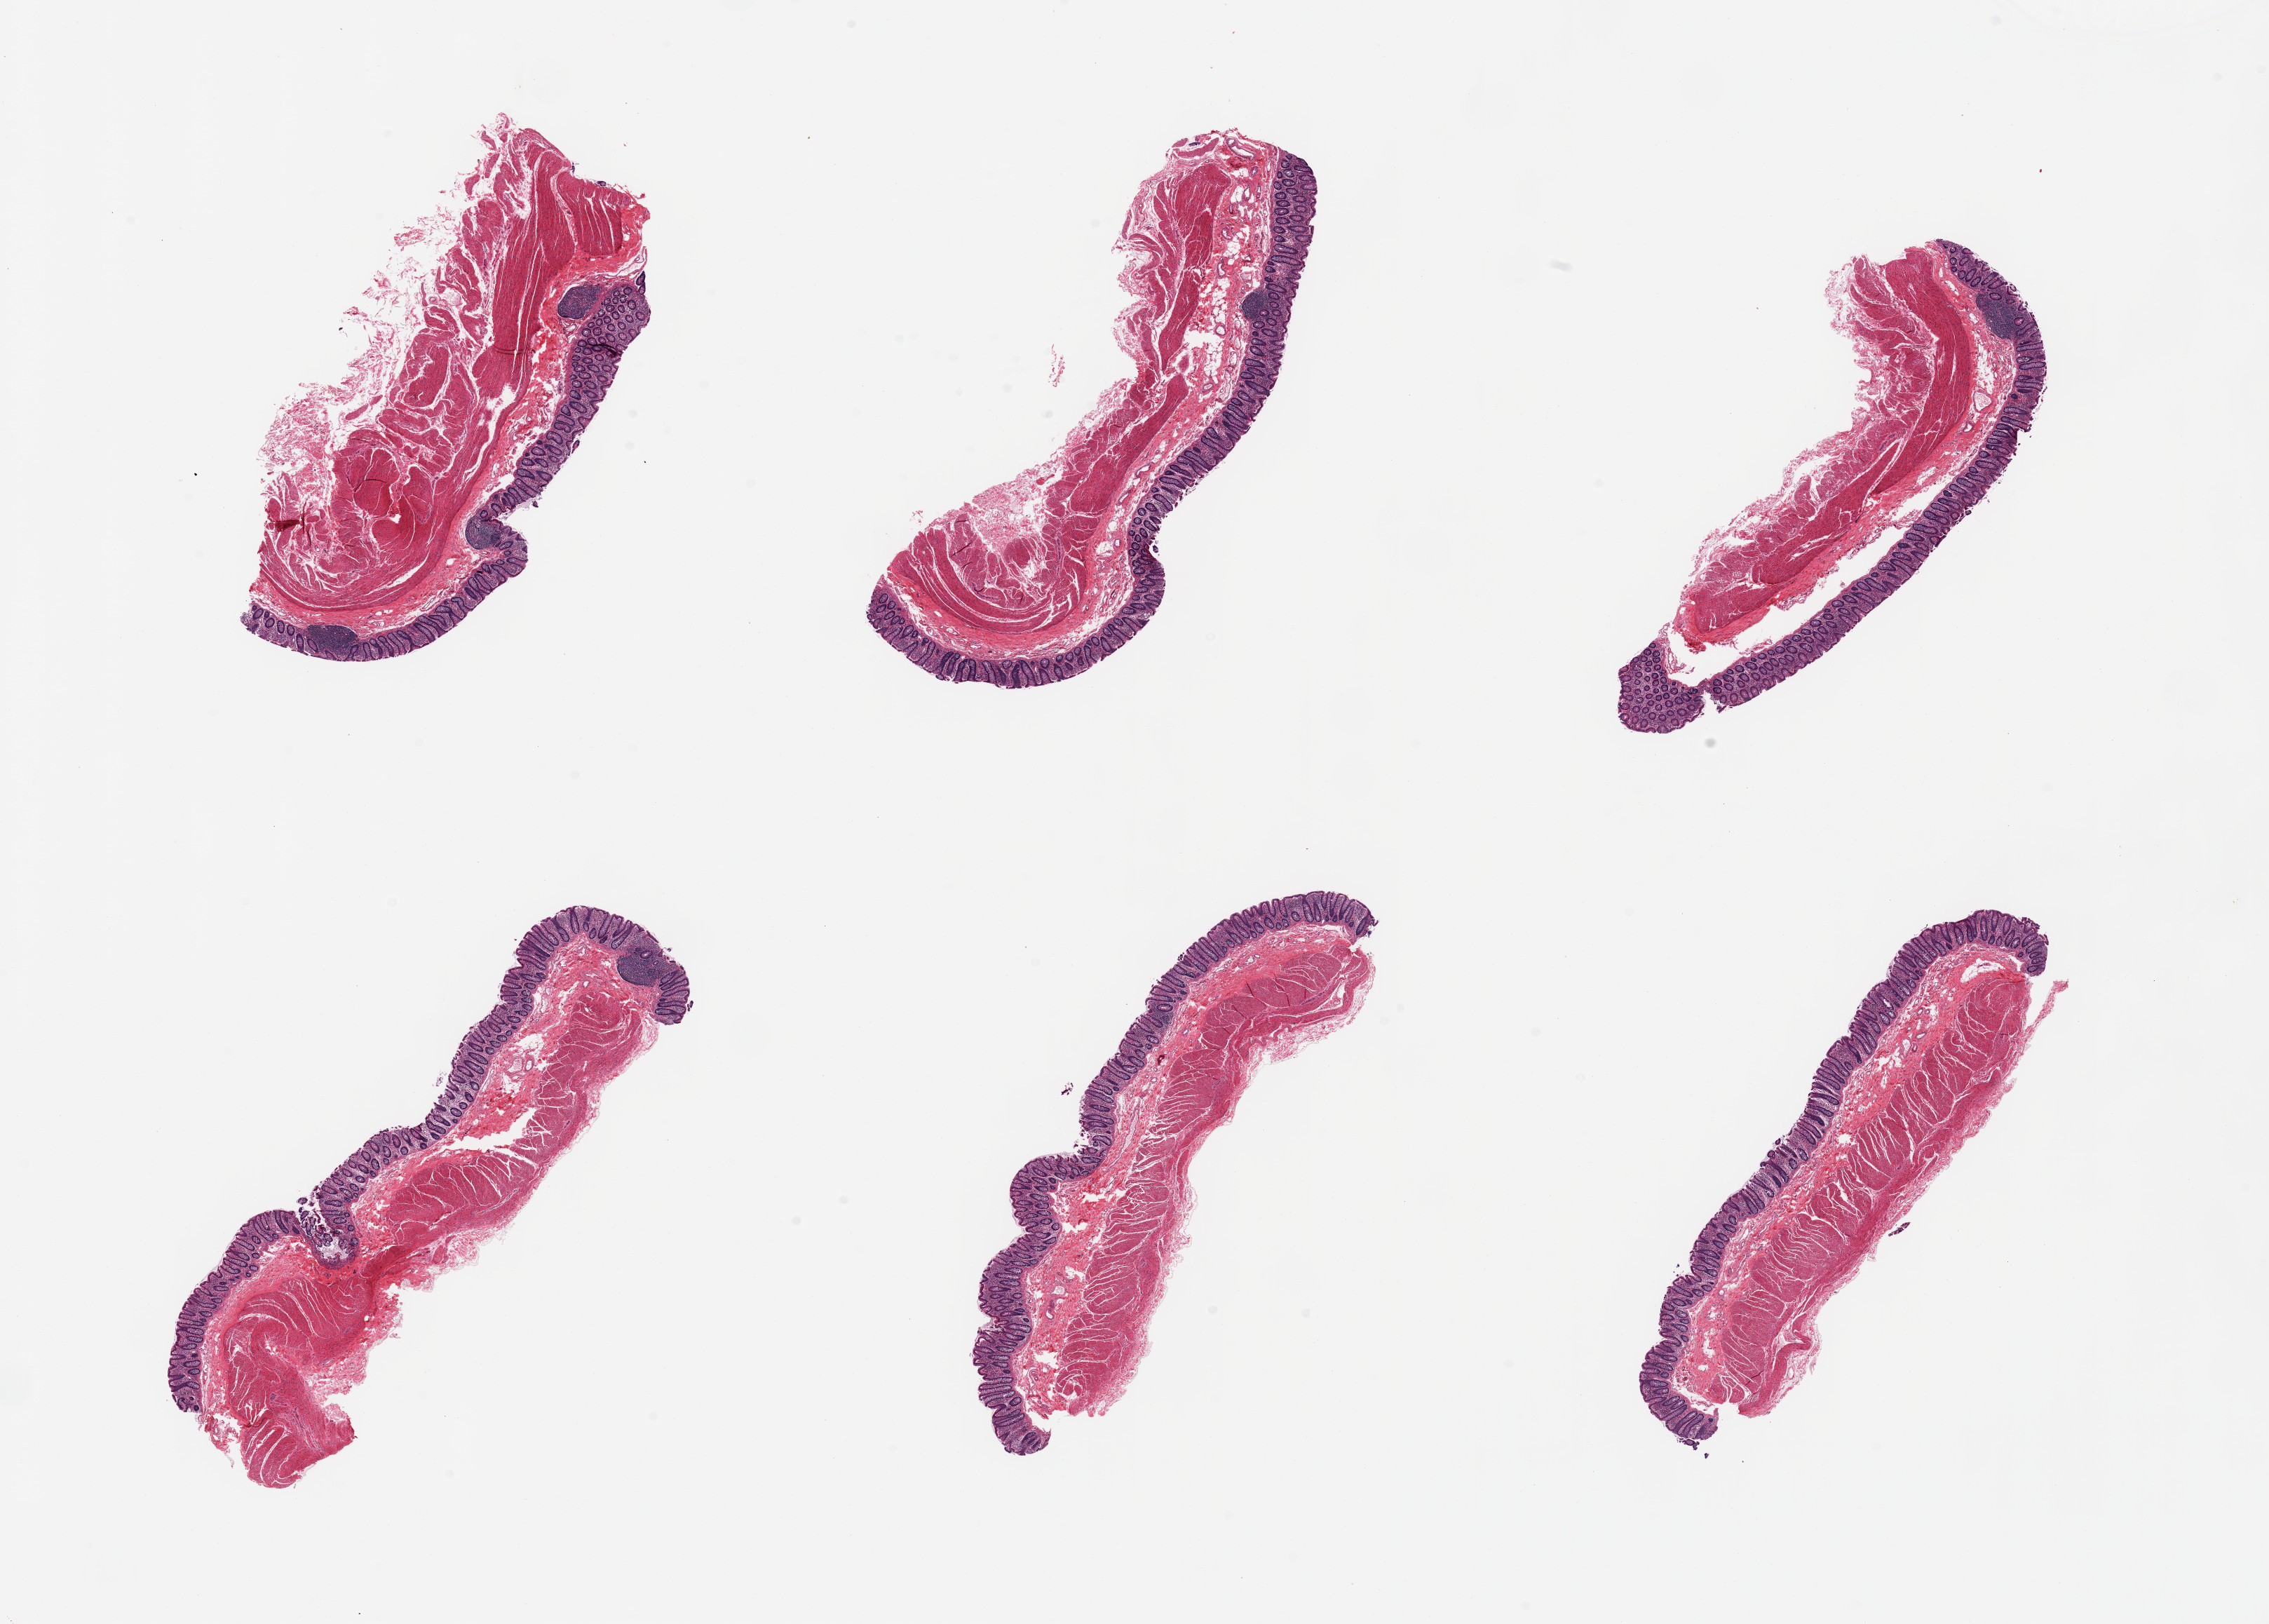
Hematoxylin and eosin (H&E) whole-slide image, brightfield, shown as a low-resolution overview of the whole scanned area (about 25.6 x 18.3 mm, from a 20x scan). PAXgene-fixed, paraffin-embedded tissue. Target tissue: transverse colon. Donor tissue sample. Donor sex: male.
Review note (as recorded): 6 pieces, mucoa well preserved, up to ~0.5mm, ~15-20% thickness.